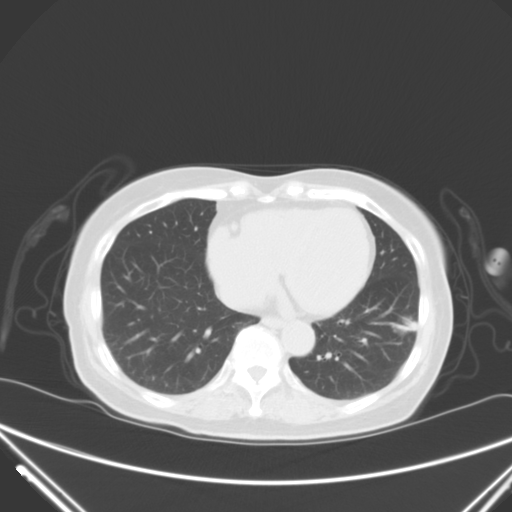
Chest CT, one axial slice. Lung window (W 1500 / L -600 HU). 5 mm slice thickness. 512 × 512 image matrix, field of view 377 × 377 mm. Patient: female, 82 years. From the clinical record (not read from this slice): clinical TNM (as recorded): T1c N0 M0; histopathological grade: G2.
Outlined on this slice (bounding box drawn by a radiologist):
- lung tumour (recorded histology: adenocarcinoma): bounding box [x1, y1, x2, y2] px = [395, 306, 427, 345]